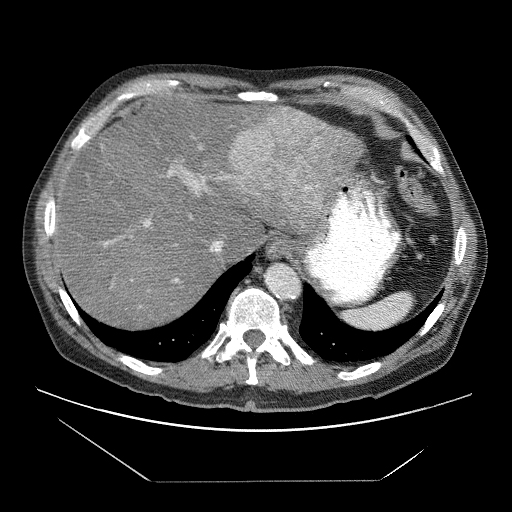
Contrast-enhanced abdominal CT (liver protocol), one axial slice; position 55 of 83 along the scan axis; 120 kVp; soft-tissue window (W 400 / L 40 HU); 2.5 mm slice thickness; 512 × 512 image matrix. From the clinical record (not read from this slice): diagnosis: hepatocellular carcinoma (patient treated with transarterial chemoembolisation; whether this scan precedes or follows treatment is not stated here); TNM stage (as recorded): Stage-IVB.
Outlined on this slice (semi-automatically segmented with operator editing):
- liver parenchyma outside the tumour (the mass and vessels are separate outlines, so this box may not span the whole liver): box from (x=52, y=95) to (x=364, y=326) px
- mass: (x=231, y=105)–(x=362, y=230)
- liver vessels: (x=54, y=147)–(x=247, y=308)